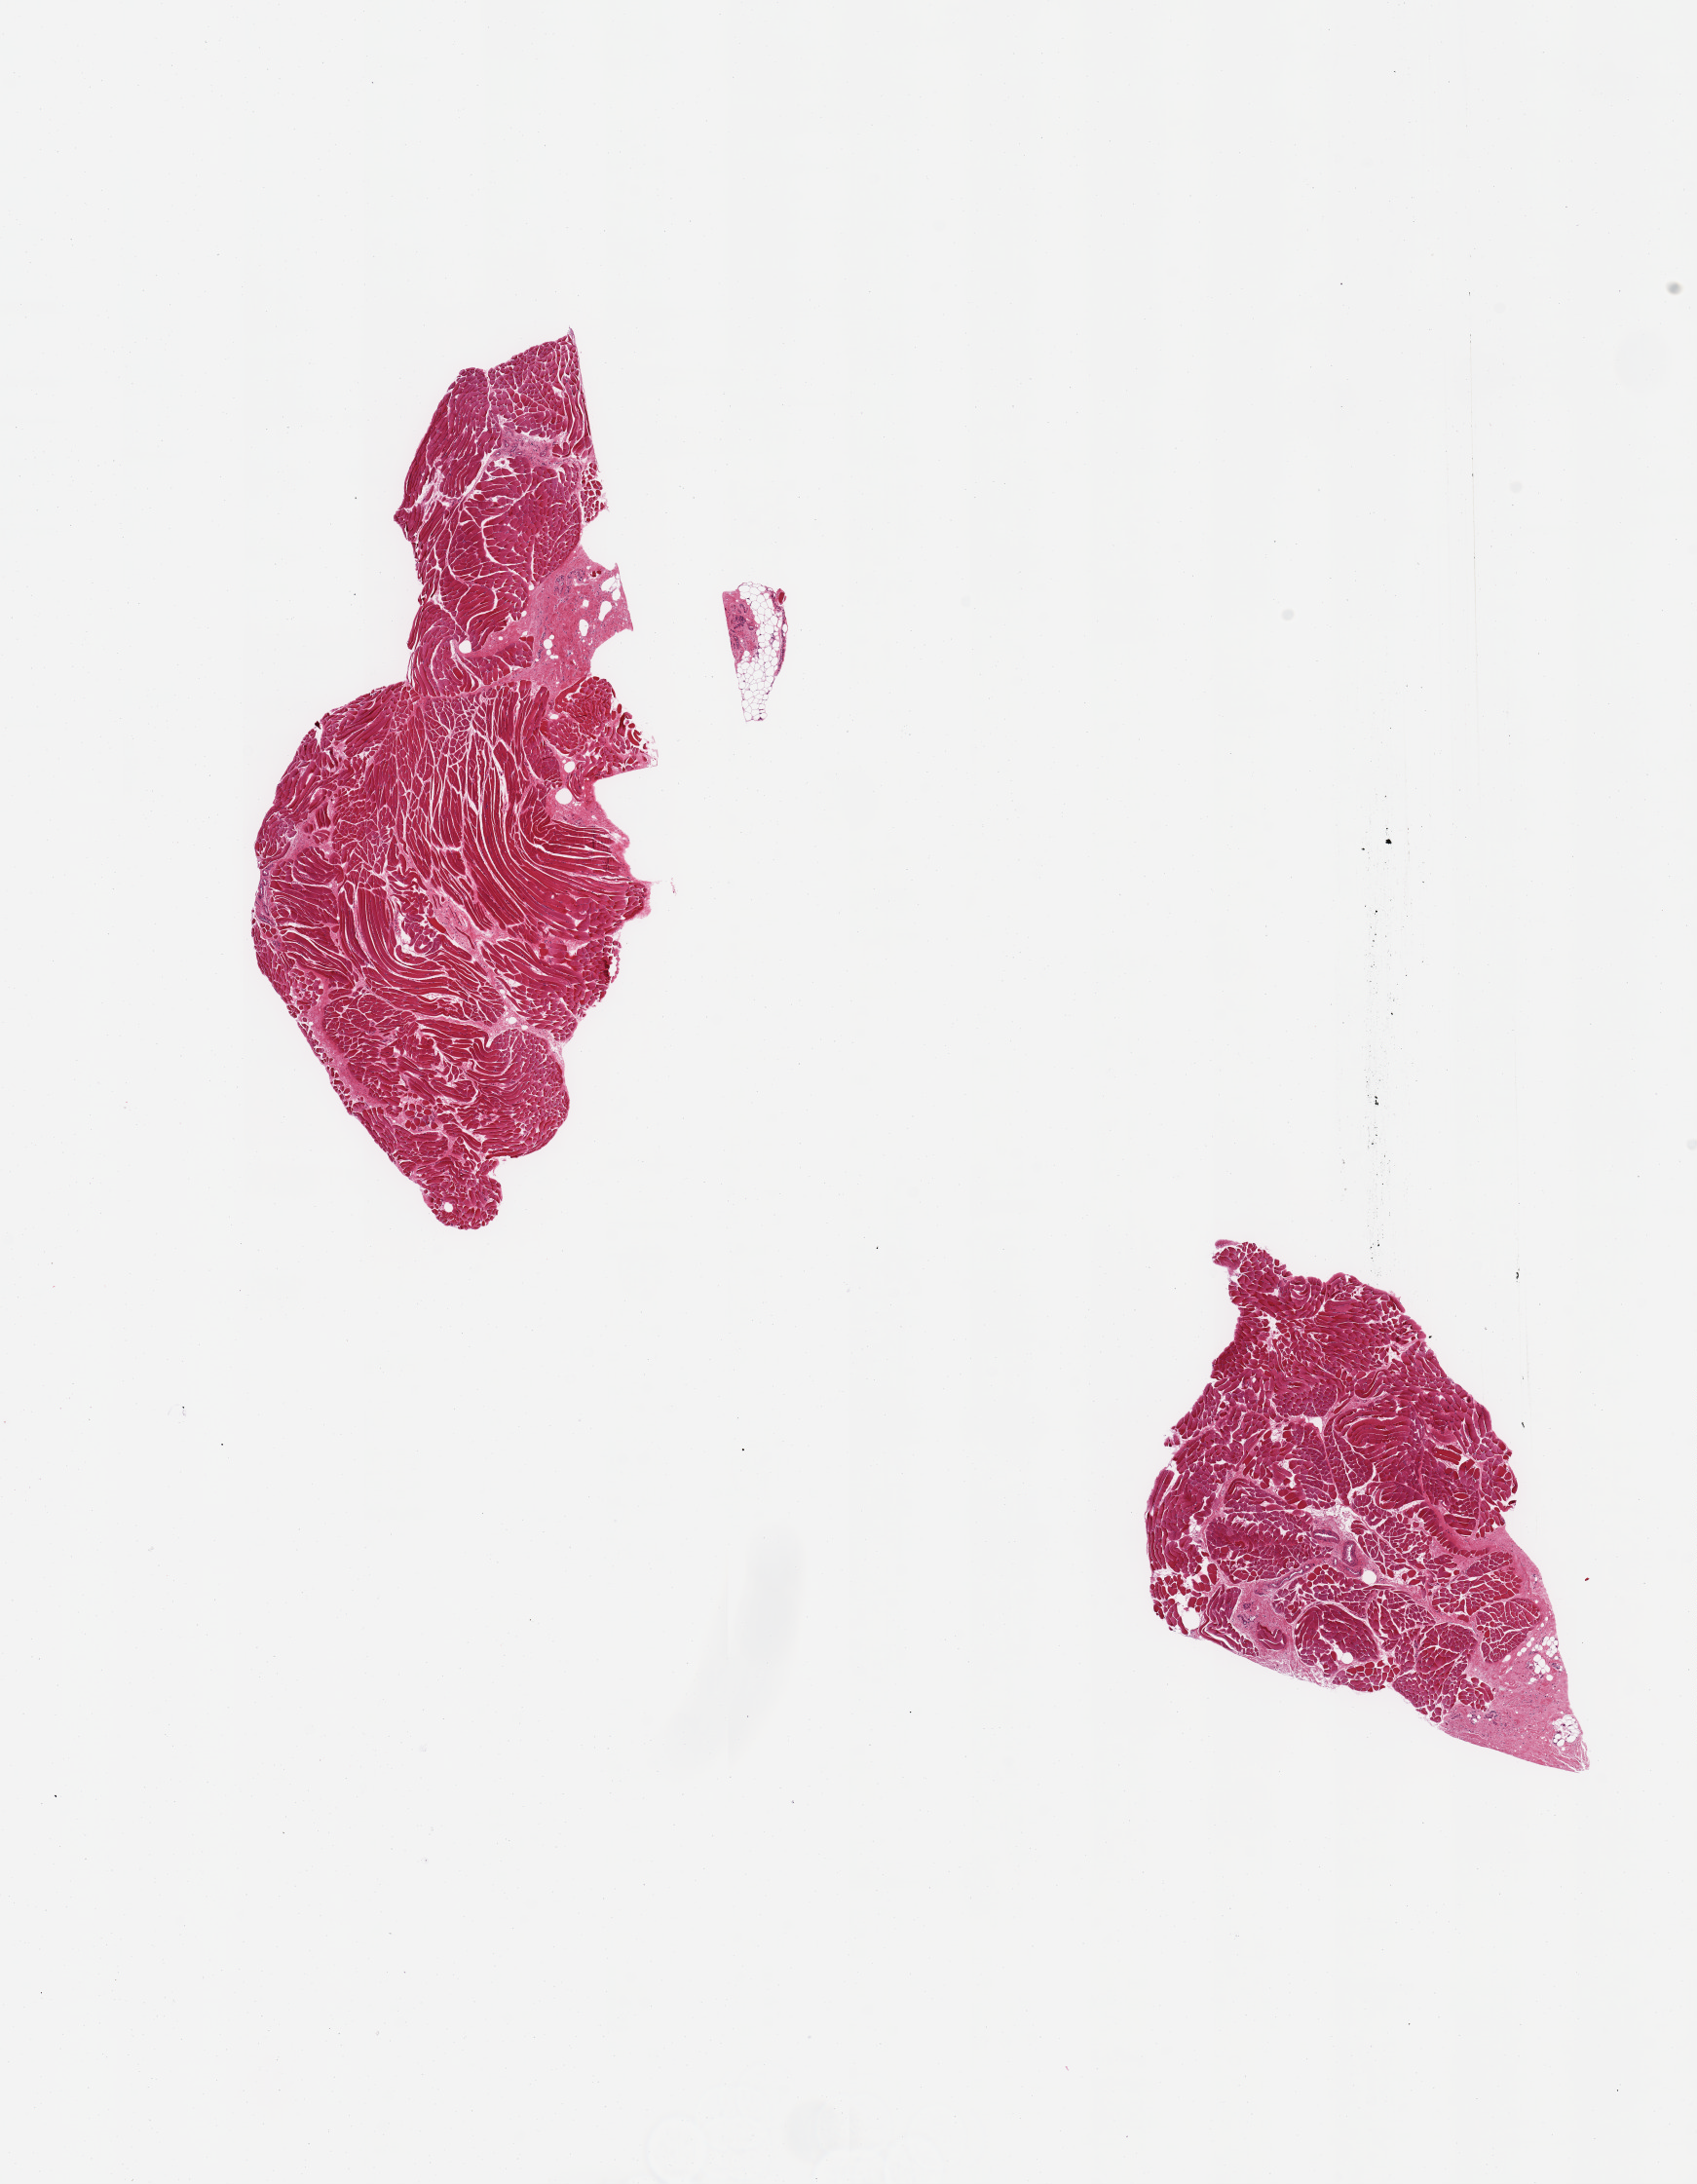
Whole-slide image, hematoxylin and eosin (H&E) stain, whole scanned area (about 13.8 x 17.7 mm) shown as a low-resolution overview. PAXgene-fixed, paraffin-embedded tissue. Sampled site (target tissue): thyroid. Donor tissue sample.
Pathologist's review note for this sample: 2 pieces; thyroid gland not present instead skeletal muscle tissue with interstitial fibrosis.